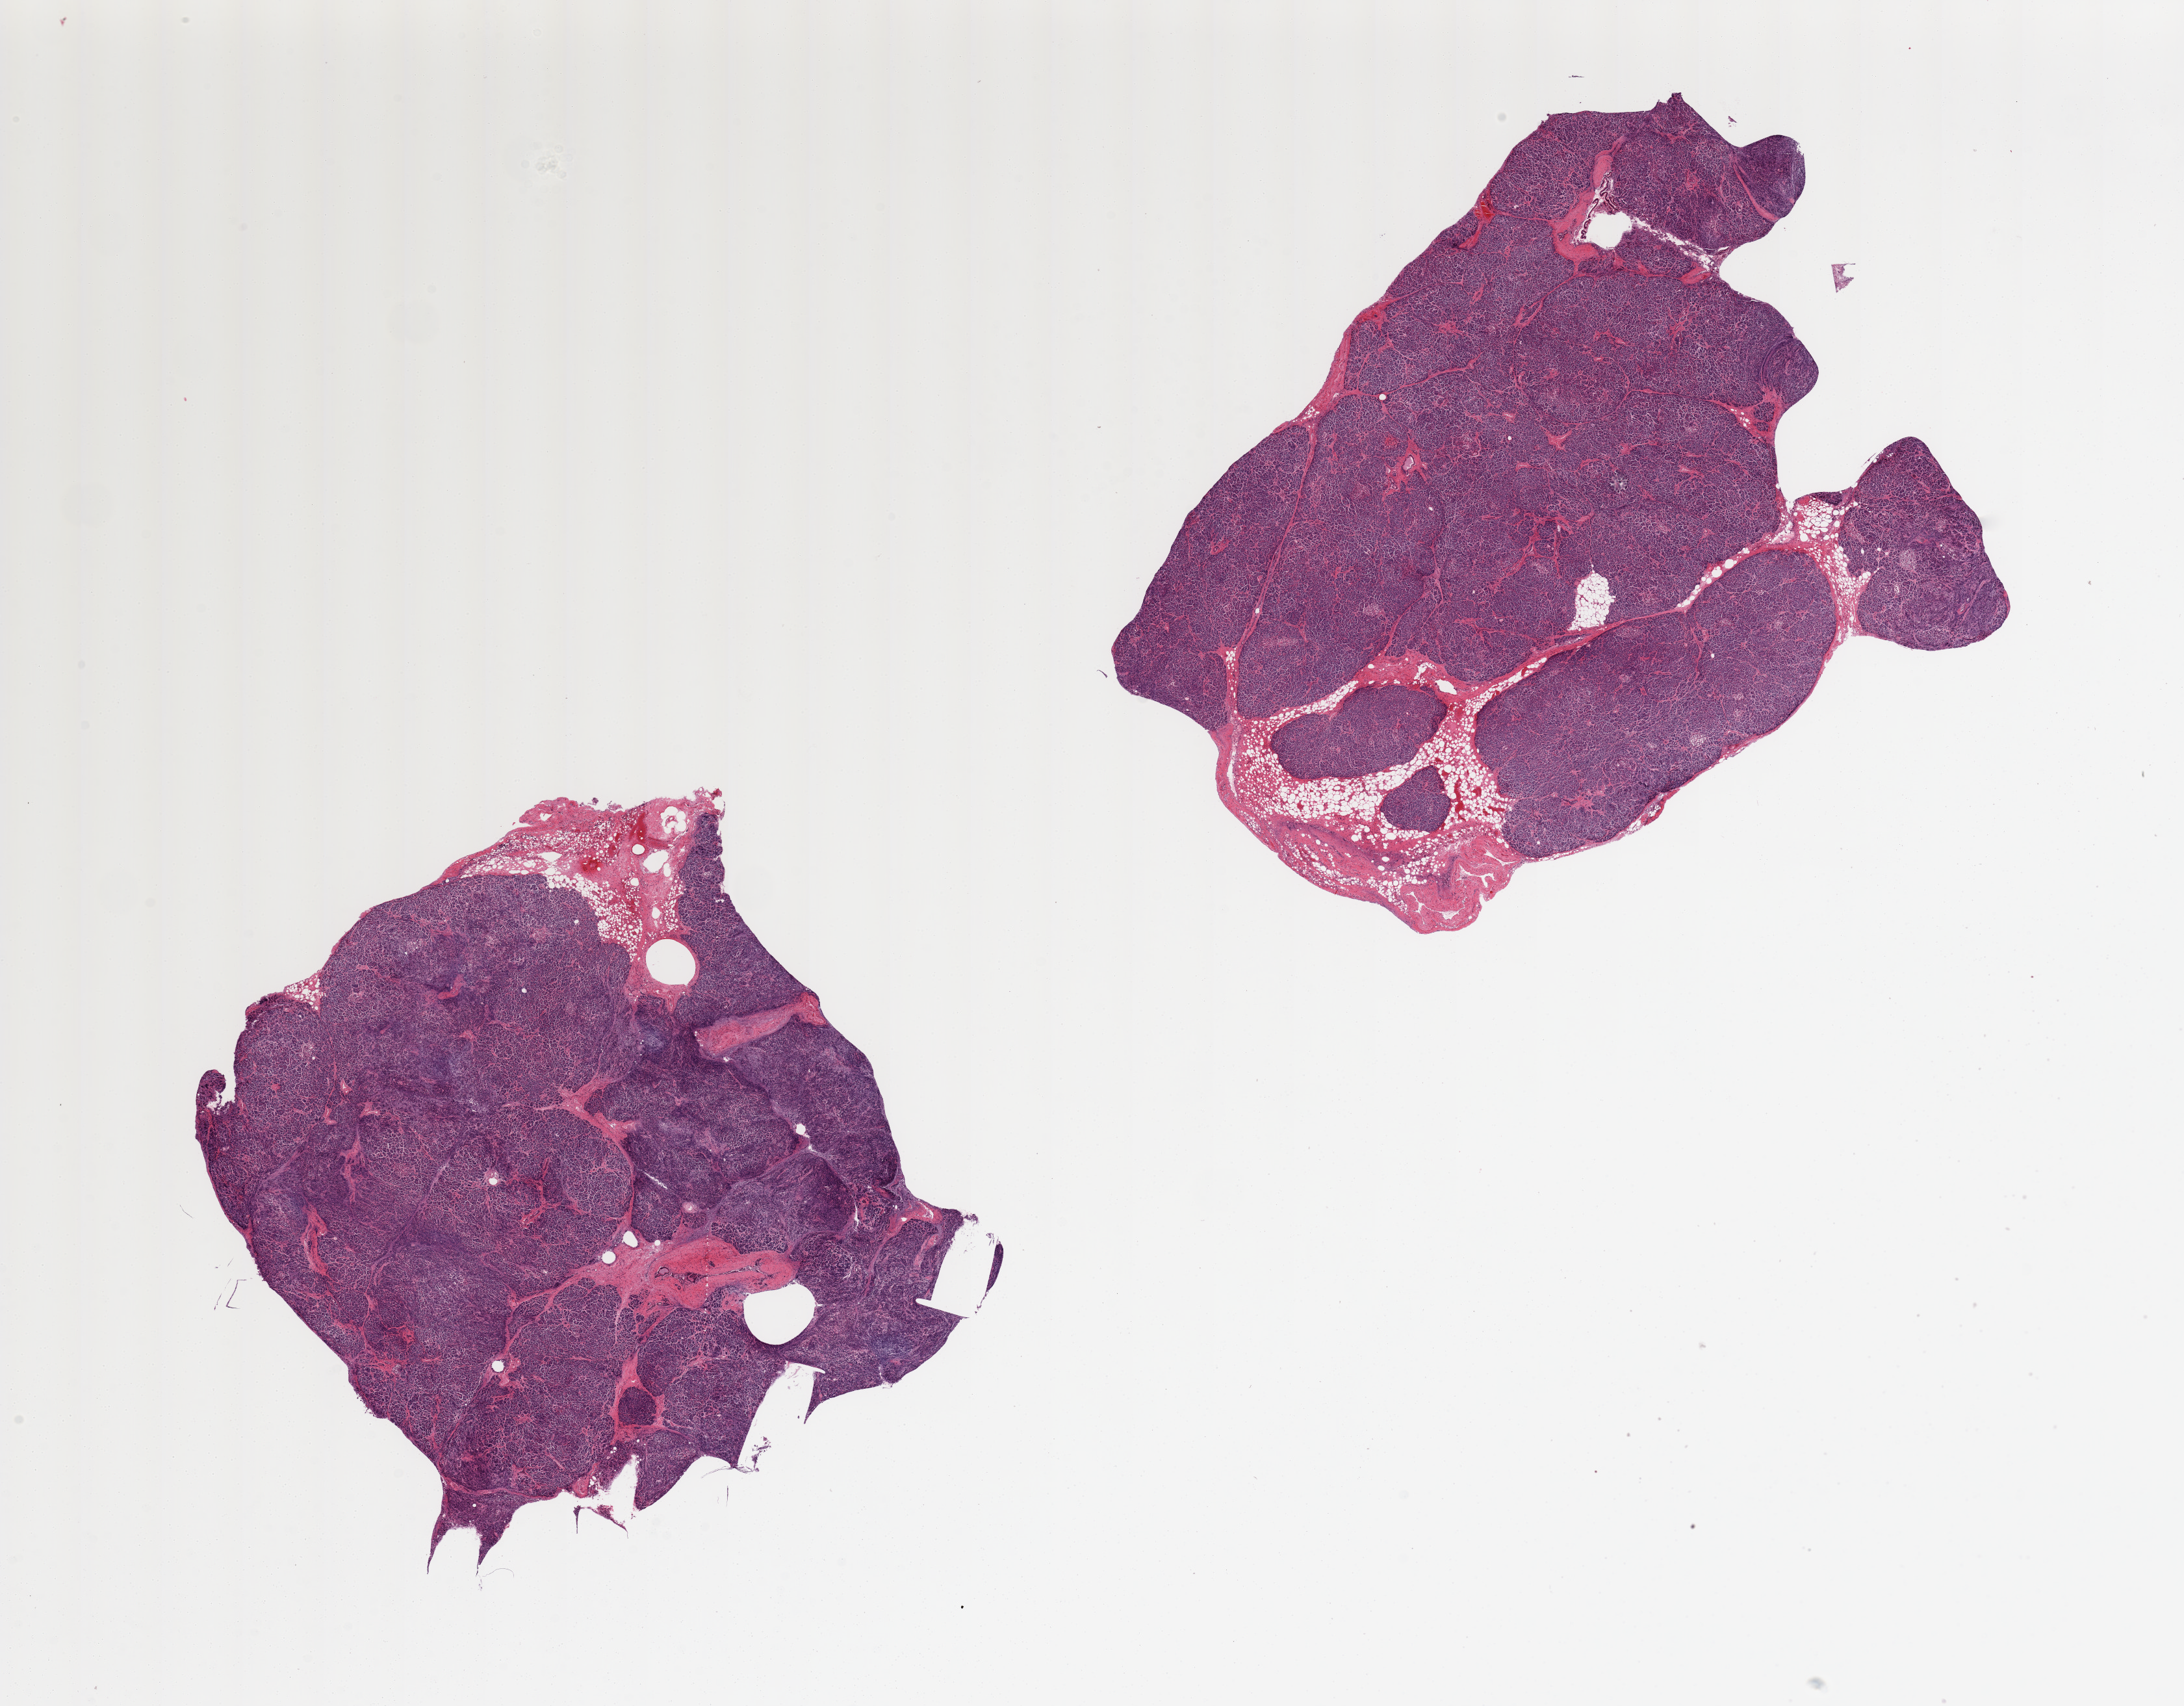
Whole-slide image, haematoxylin and eosin stain, low-resolution overview of the scanned area, about 26.6 x 20.8 mm. PAXgene-fixed paraffin-embedded (PFPE) section. Sampled site (target tissue): pancreas. Tissue donor sample. Donor sex: male.
Review note (as recorded): 2 pieces, moderate autolysis/saponfication.